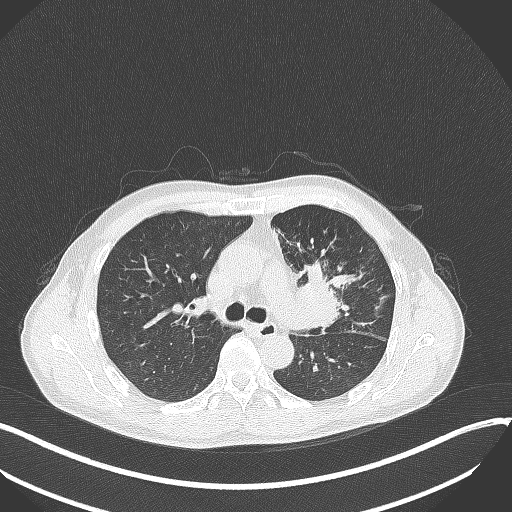
Chest CT, one axial slice. Slice 218 of 411 in the series (ordered by position). Lung window (W 1500 / L -600 HU). 512 × 512 image matrix, field of view 400 × 400 mm. Male patient, age 56 years. Case-level facts recorded for this patient, not image findings: clinical TNM (as recorded): T2a N0 M0.
Annotated regions visible in this slice (bounding box drawn by a radiologist):
- lung tumour (recorded histology: squamous cell carcinoma): bounding box <294,258,347,336> (left, top, right, bottom; pixels)